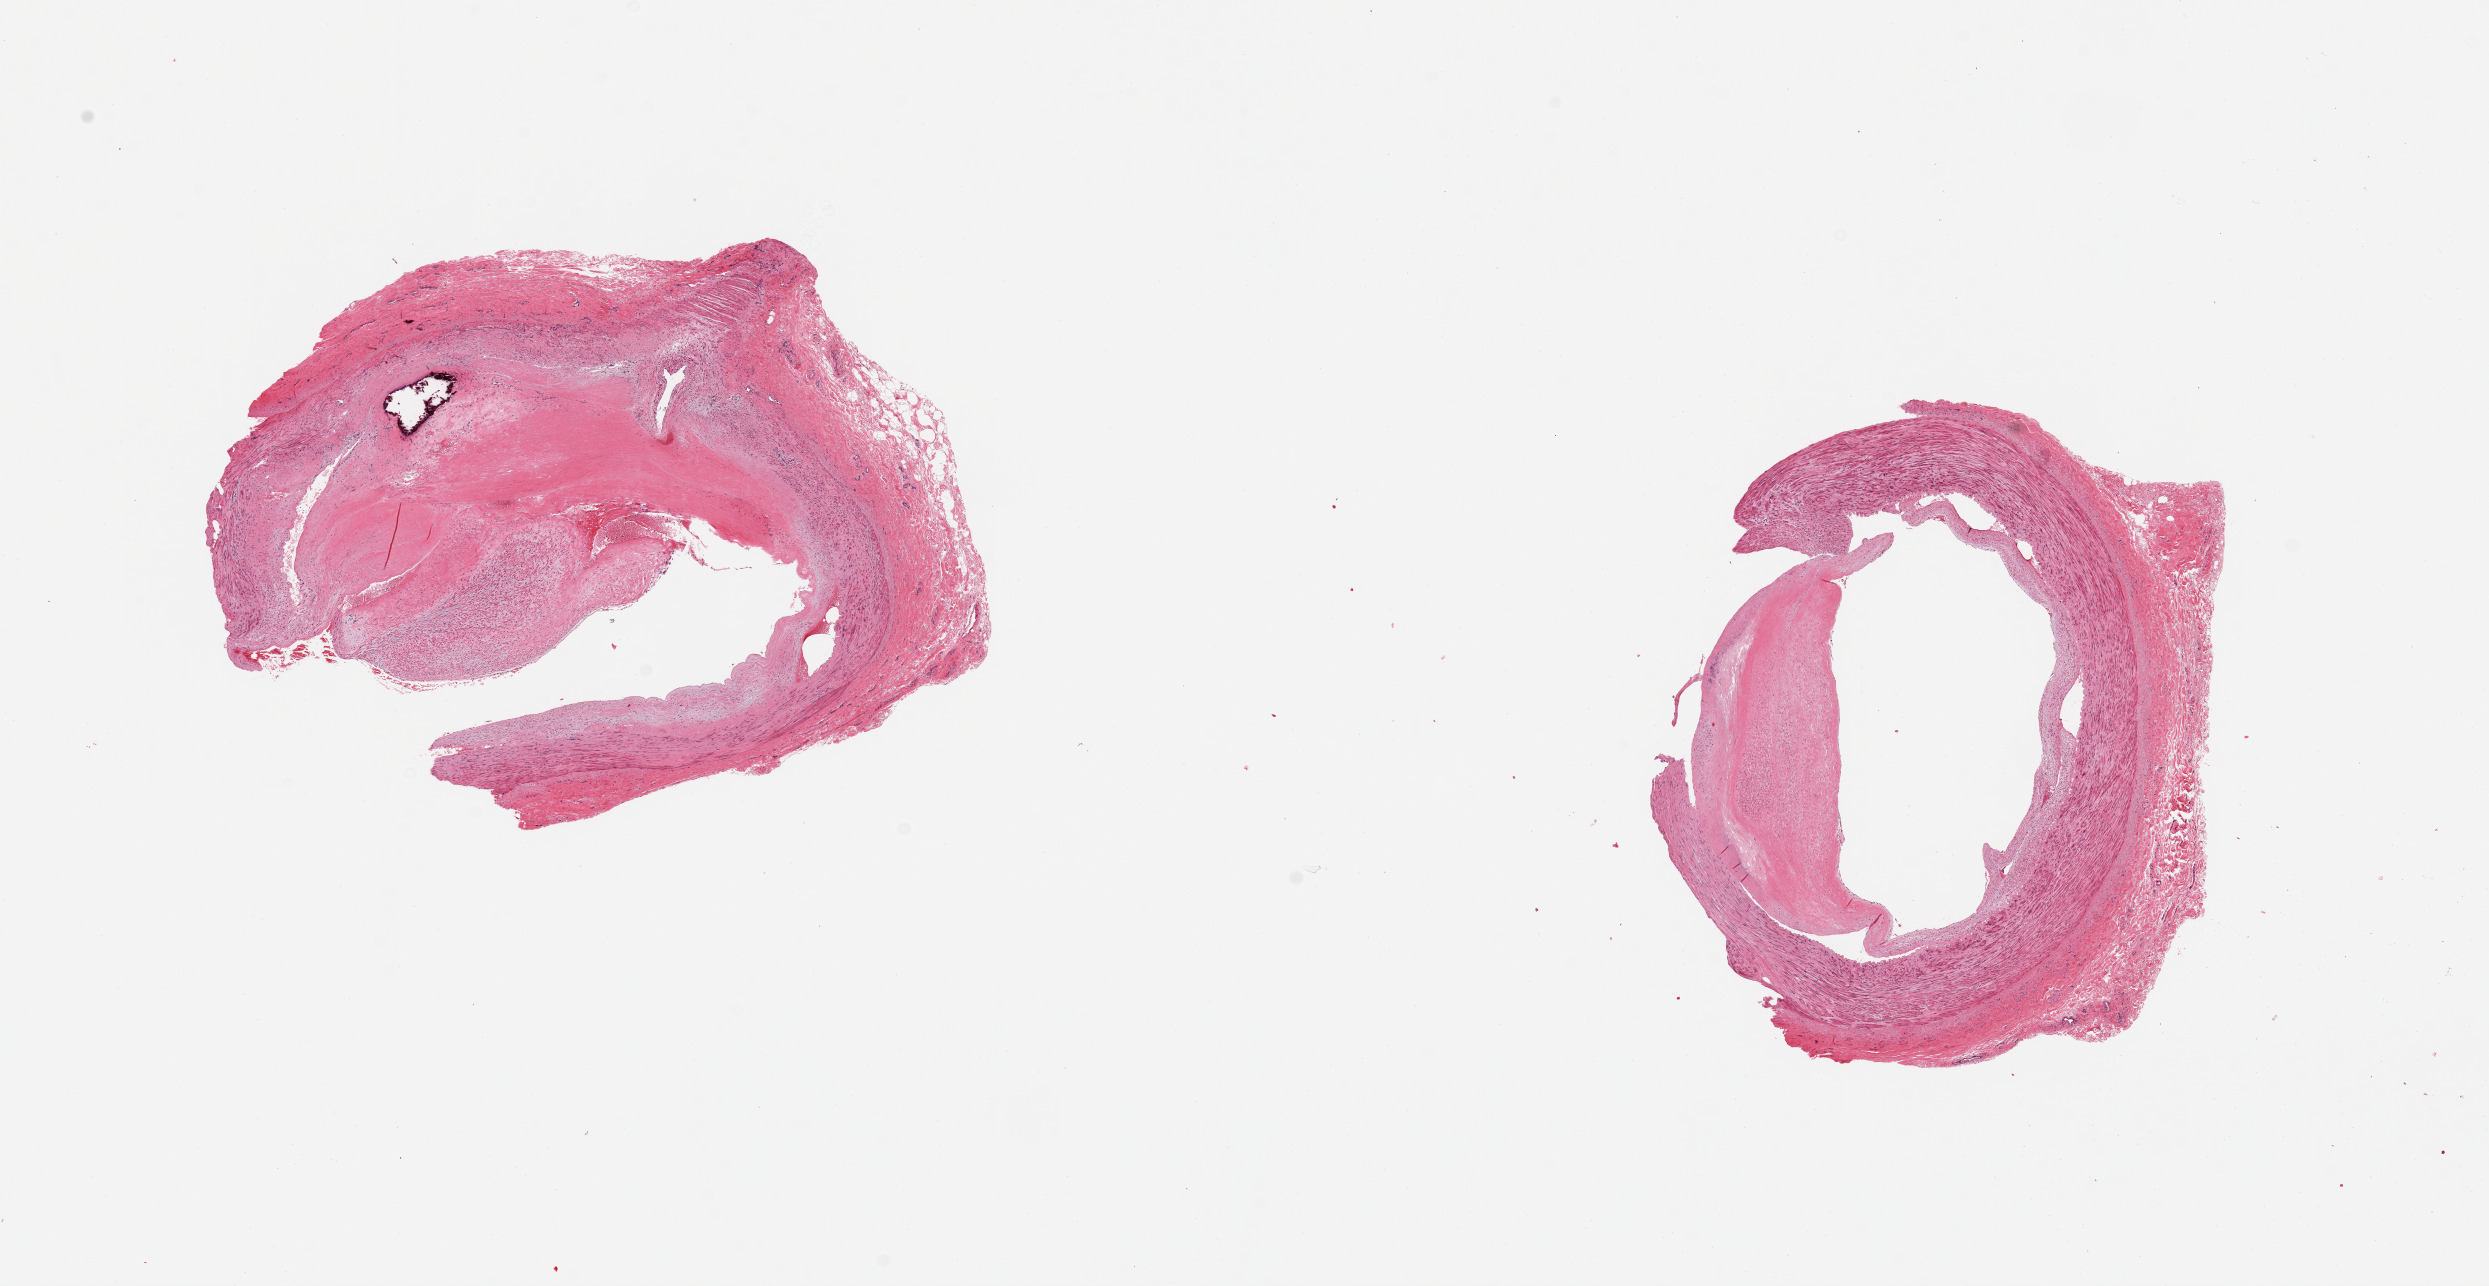
Digitized haematoxylin and eosin-stained section, brightfield, a low-resolution overview of the entire scanned area, about 19.7 x 10.2 mm, PAXgene-fixed, paraffin-embedded tissue, target tissue: tibial artery, donor tissue sample. Donor sex: female.
• review note (as recorded): 2 pieces, calcific atherosclerosis with narrowing of the lumen